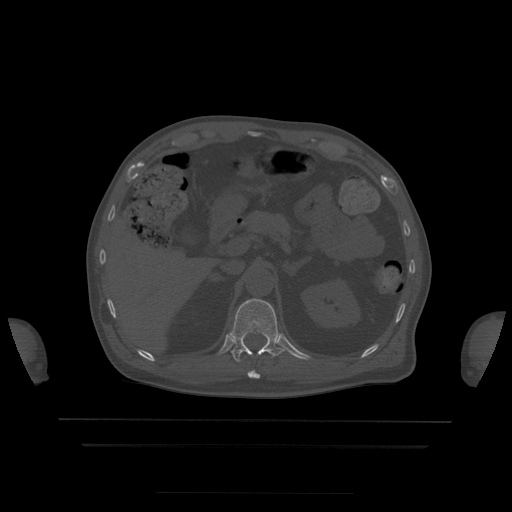
CT including the spine, one axial slice; position 199 of 522 along the scan axis; bone window (W 1800 / L 400 HU); 1.25 mm slice thickness; 512 × 512 image matrix, field of view 436 × 436 mm. Patient age 68 years. Case-level facts recorded for this patient, not image findings: primary cancer: urothelial.
Outlined on this slice (semi-automatically segmented with operator editing):
- T11 vertebra: bounding box (x1, y1, x2, y2) in pixels: (248, 371, 261, 379)
- T12 vertebra: (229, 299, 284, 362)